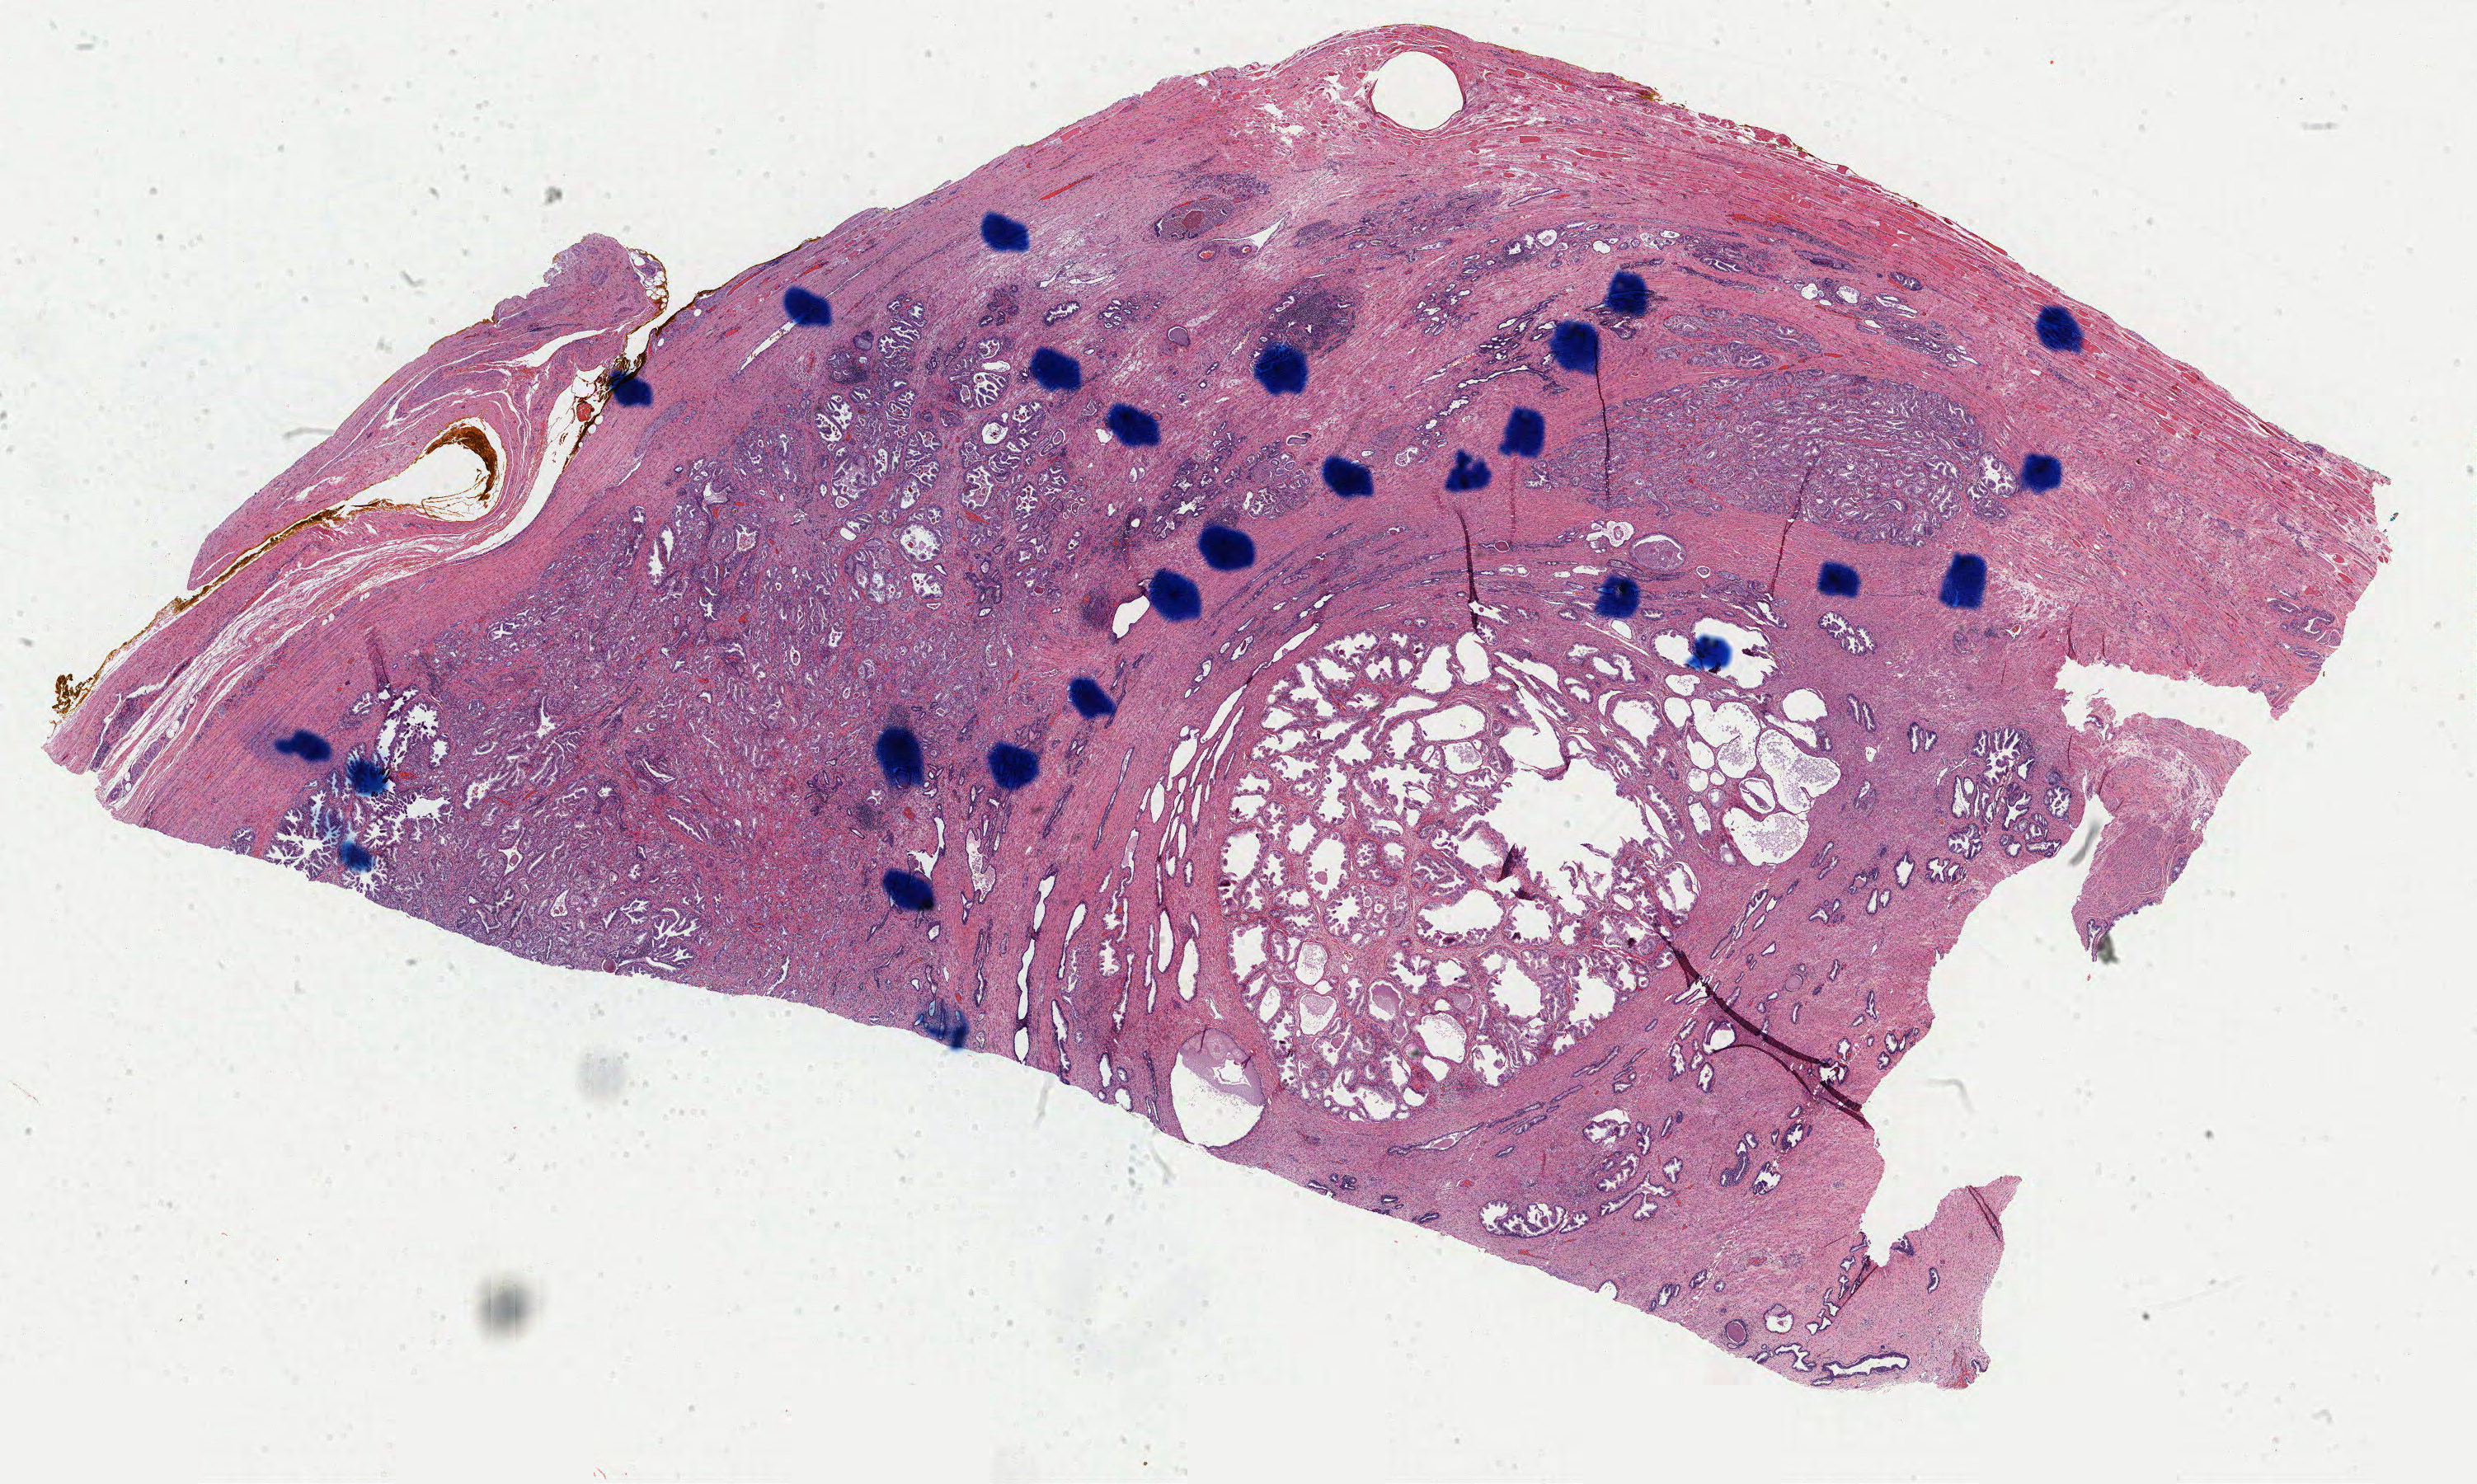
H&E whole-slide image, shown as a low-resolution overview of the whole scanned area (about 23.8 x 14.3 mm); formalin-fixed paraffin-embedded (FFPE) diagnostic section; prostate, primary tumour sample. Male, age 58 years at initial diagnosis. Gleason score: 7 (3+4).
- pathologic diagnosis: Adenocarcinoma, NOS